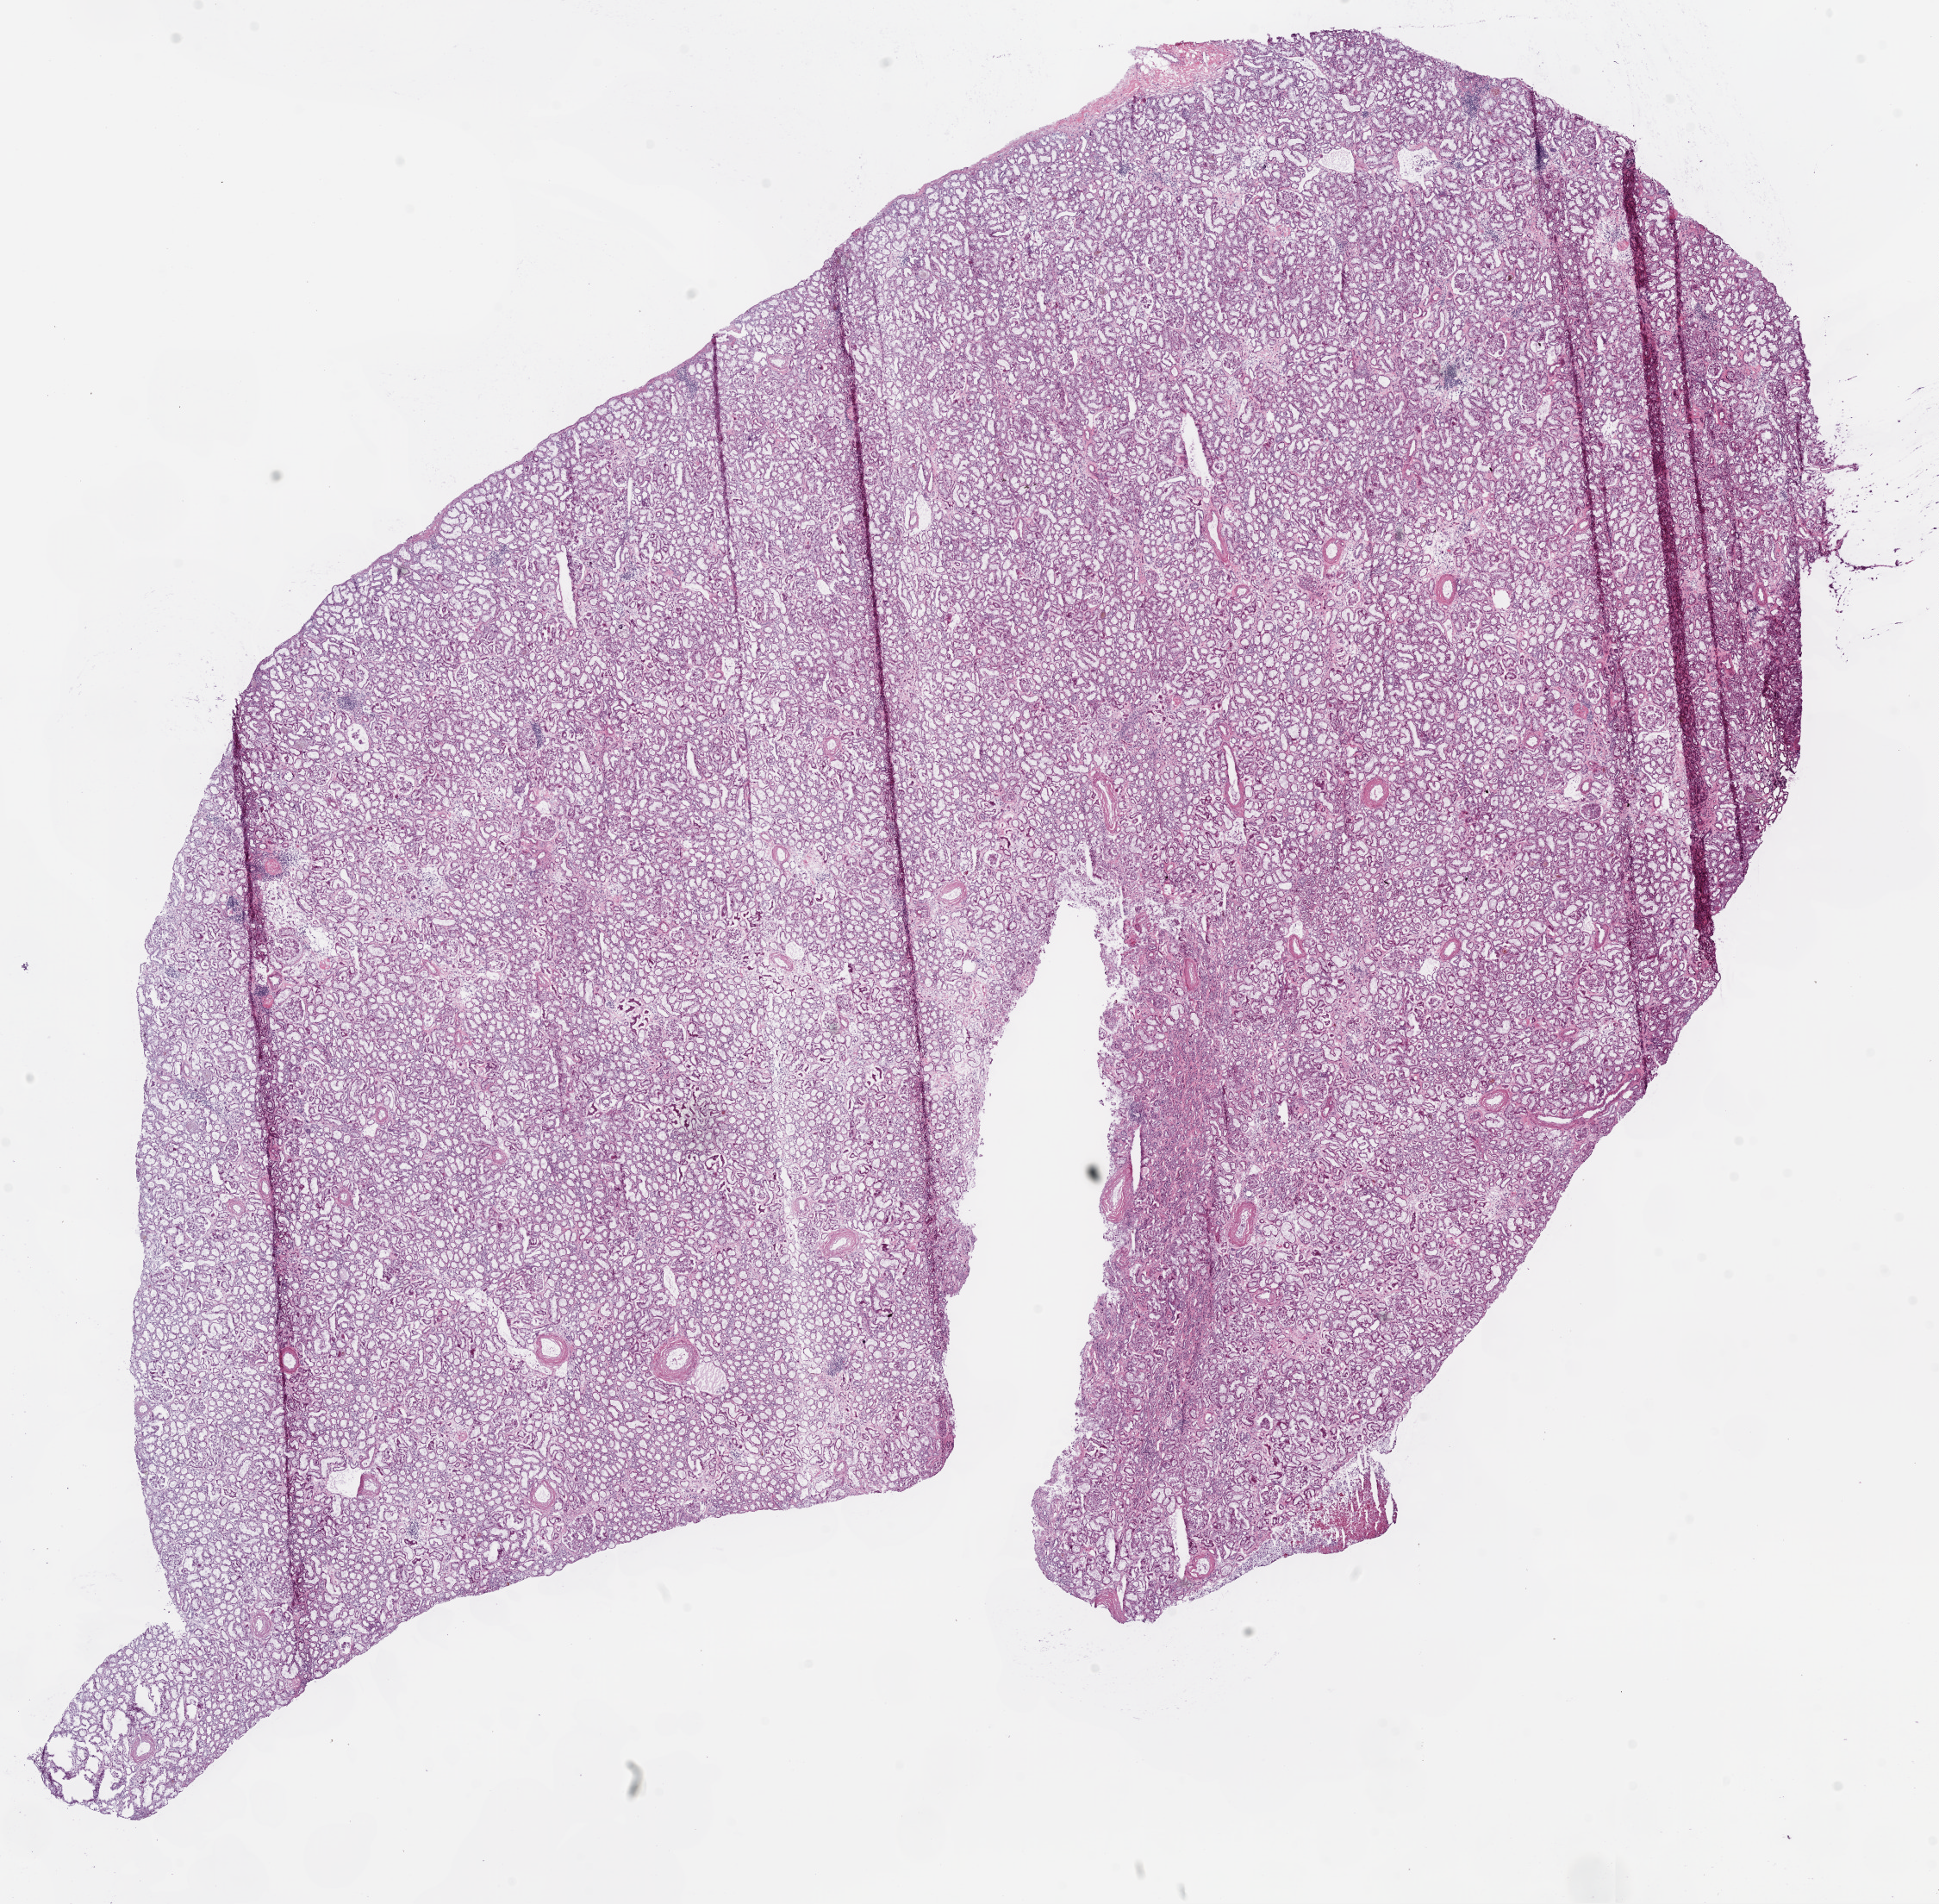
Digitized Hematoxylin and eosin (H&E) stained tissue section (whole slide), whole scanned area (about 18.1 x 17.7 mm) shown as a low-resolution overview; frozen section from the bottom of the tissue portion; sample: solid tissue normal (non-tumour tissue), kidney. Male, age 75 years at initial diagnosis.
This section: solid tissue normal (non-tumour) sample from the same patient. Patient diagnosis: Clear cell adenocarcinoma, NOS.